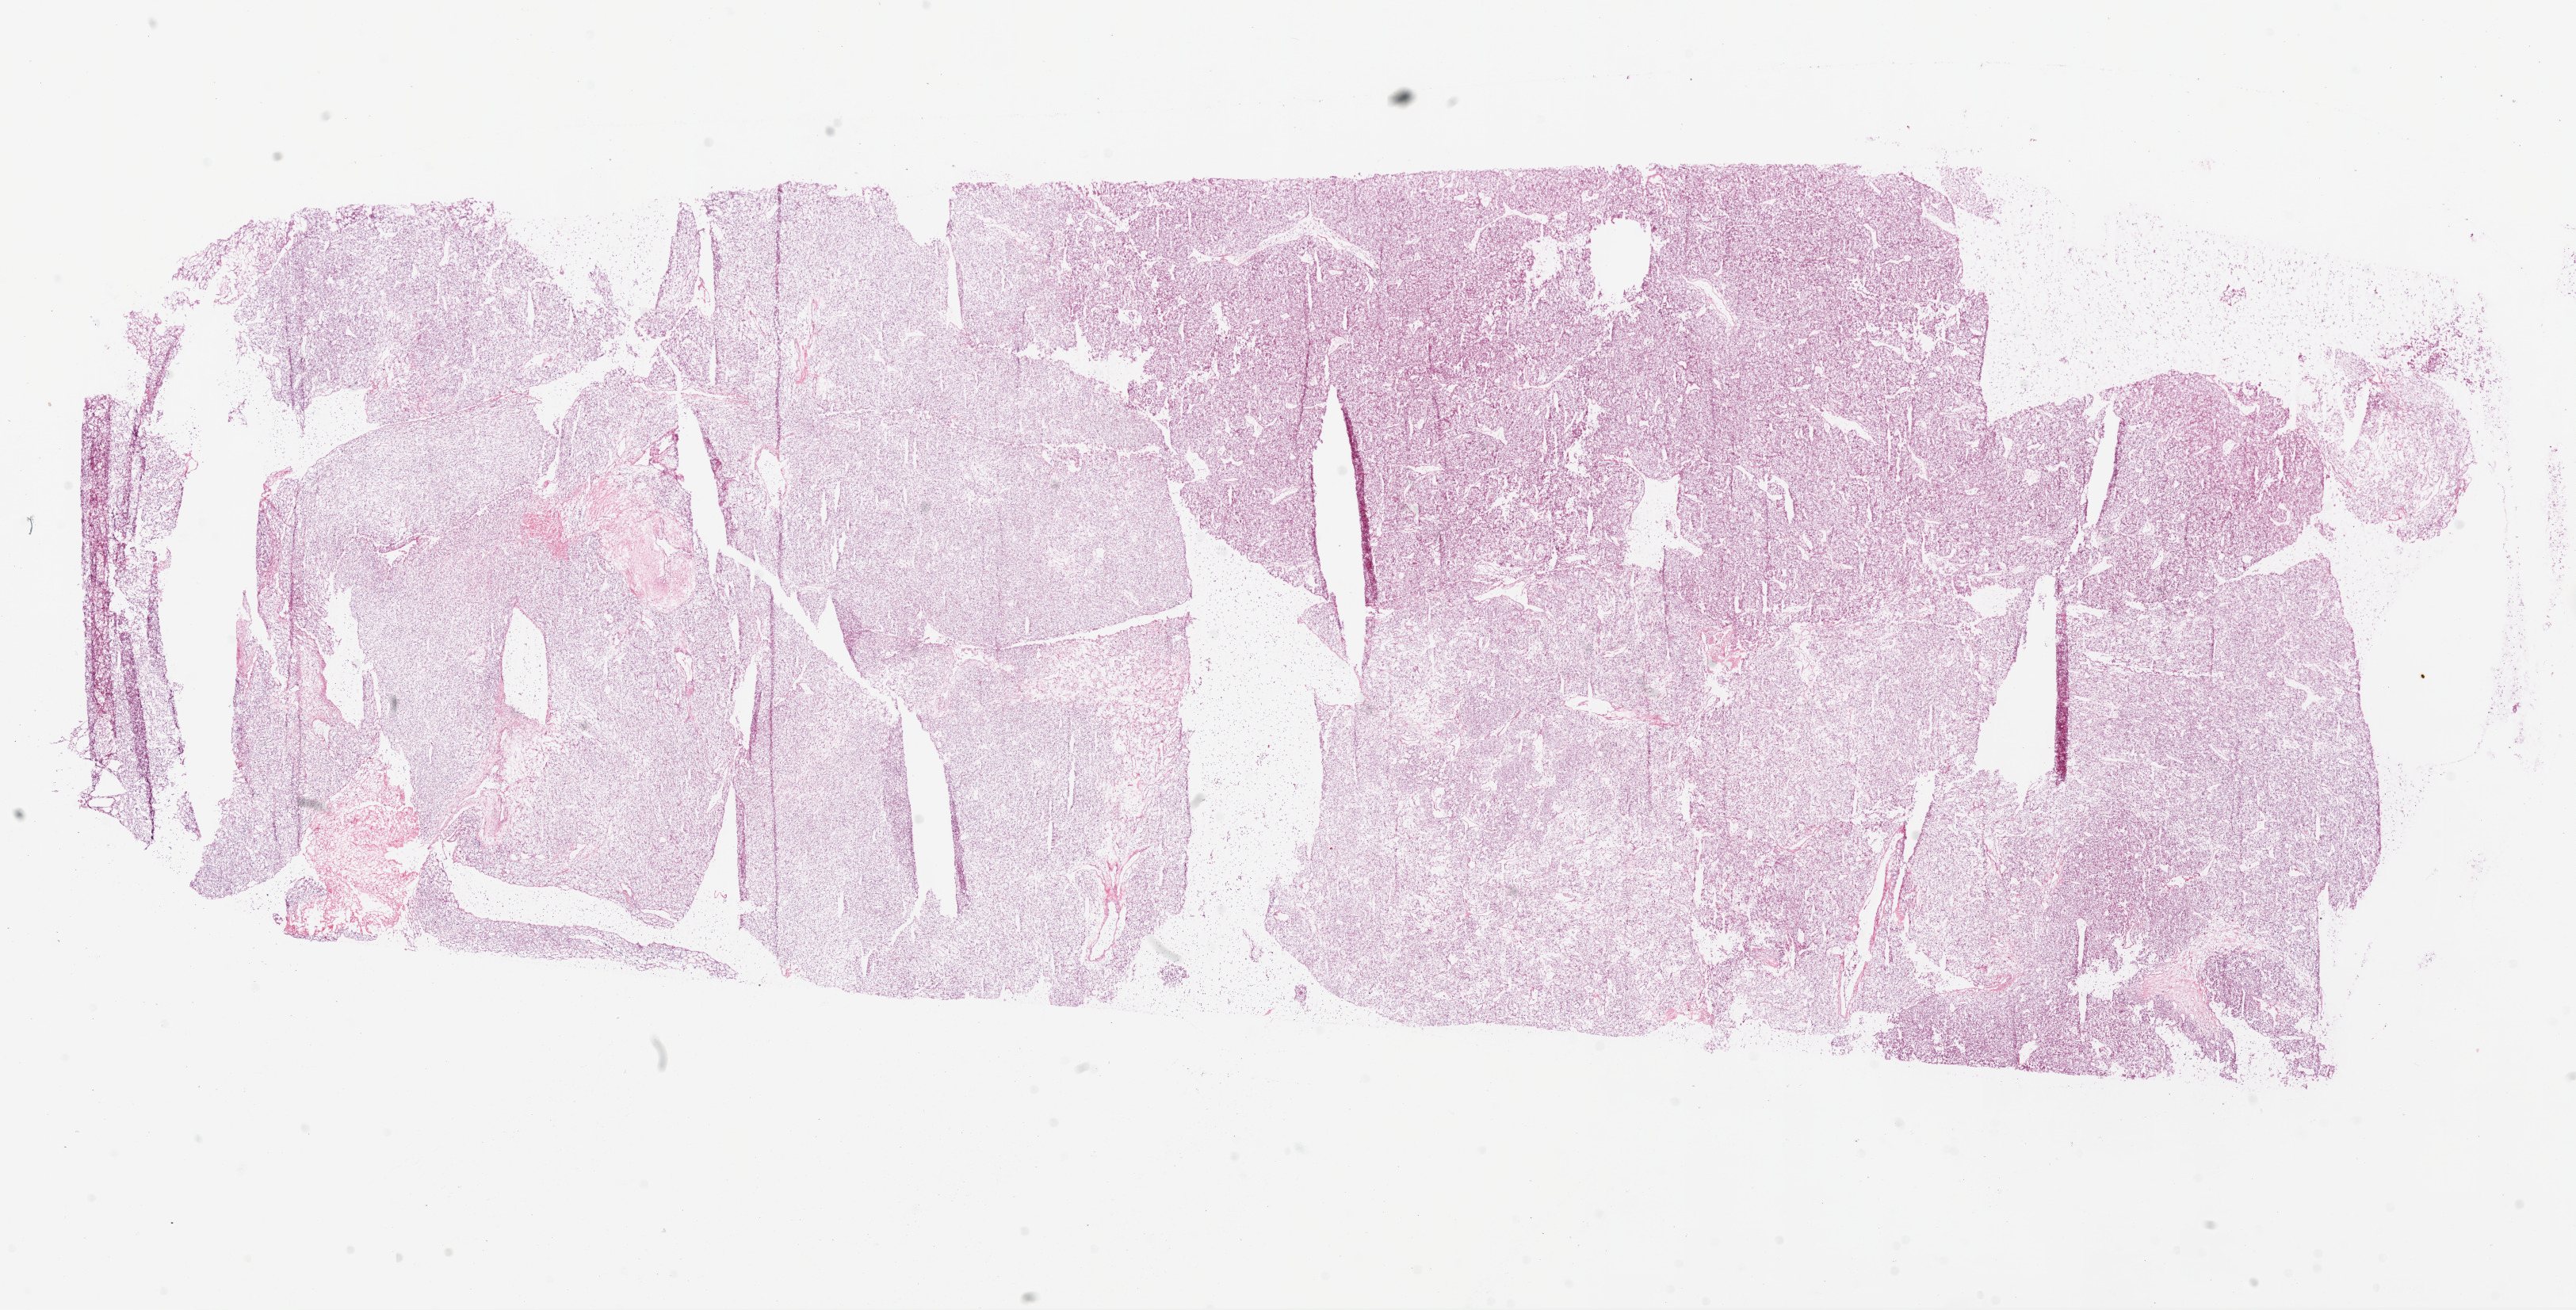
Whole-slide histology image, H&E, low-resolution overview of the scanned area, about 26.1 x 13.3 mm (acquisition: 20x scan). Frozen section. Sample: primary tumour, kidney. Female patient; age at initial diagnosis 48 years. Histologic grade: G3 (poorly differentiated). Composition of this section per pathologist review: tumour cells 95%, tumour nuclei 85%, normal cells 0%, stromal cells 5%, necrosis 0%.
* AJCC pathologic stage: IV
* diagnosis: Clear cell adenocarcinoma, NOS
* laterality: left